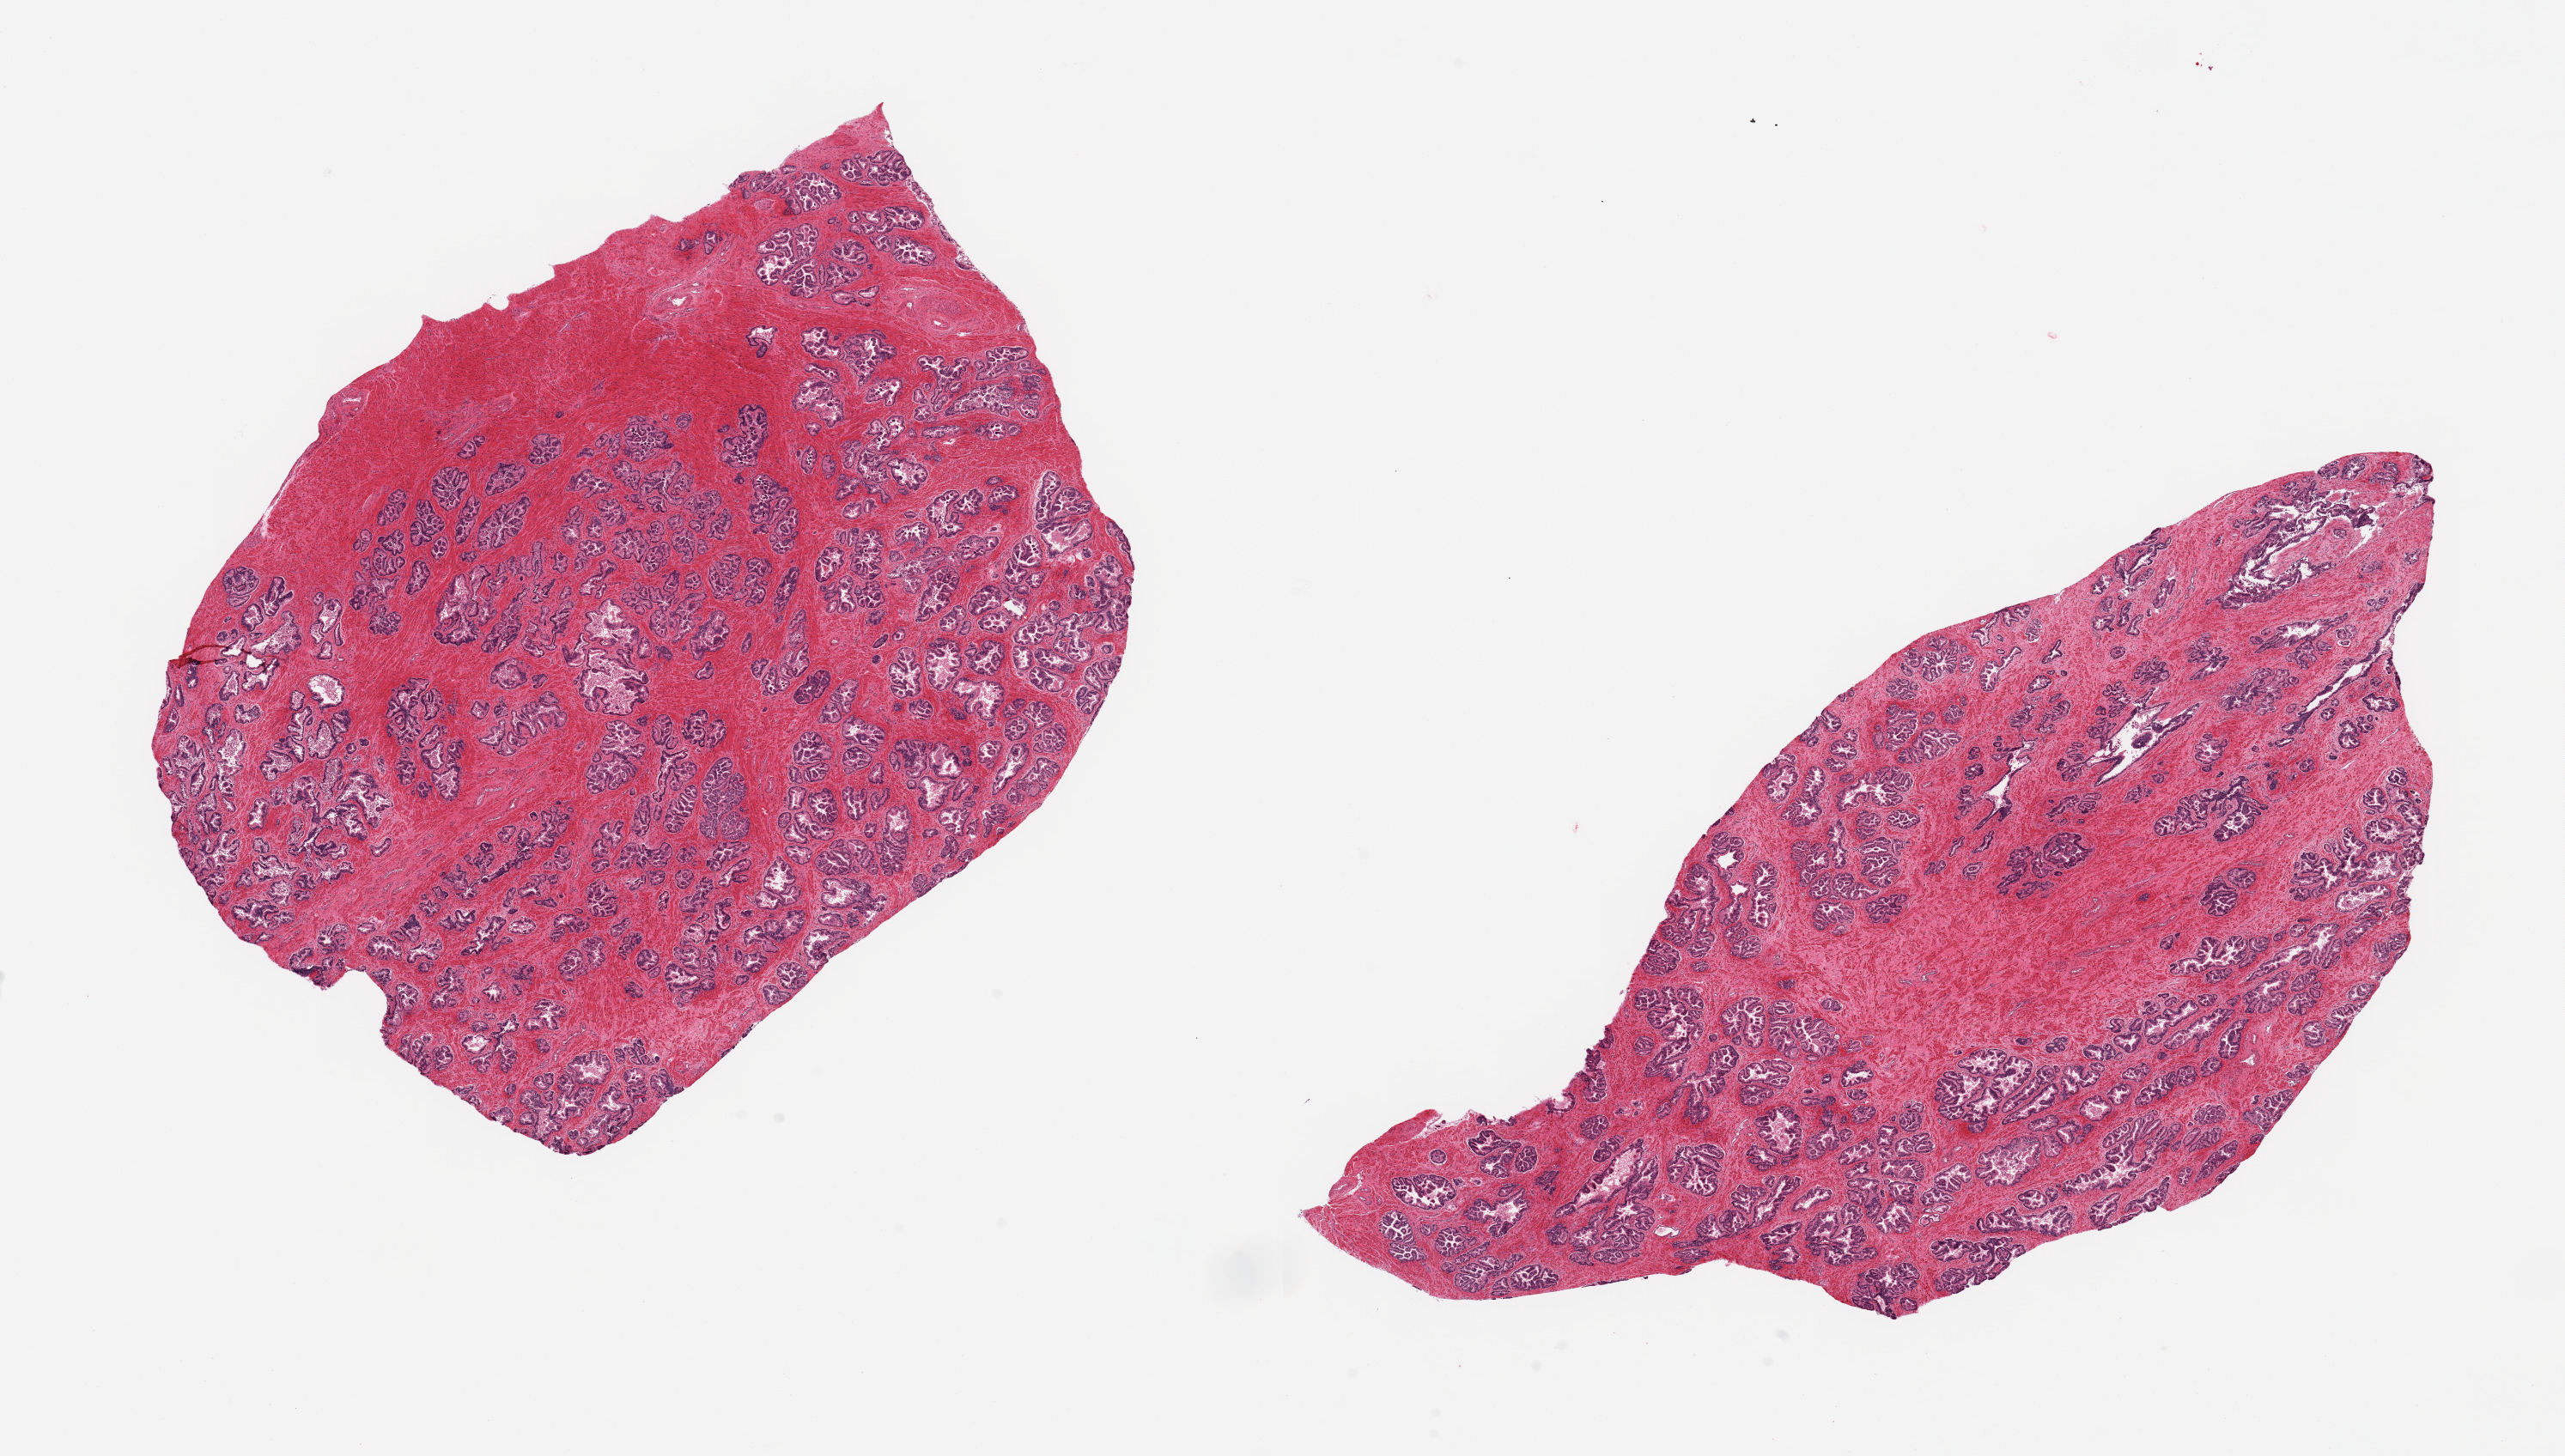
Digitized hematoxylin and eosin (H&E)-stained section, a low-resolution overview of the entire scanned area, about 23.6 x 13.4 mm. PAXgene-fixed, paraffin-embedded tissue. Sampled site (target tissue): prostate. Donor tissue sample. Donor sex: male.
• pathologist's review note for this sample: 2 pieces; admixed stroma and glands